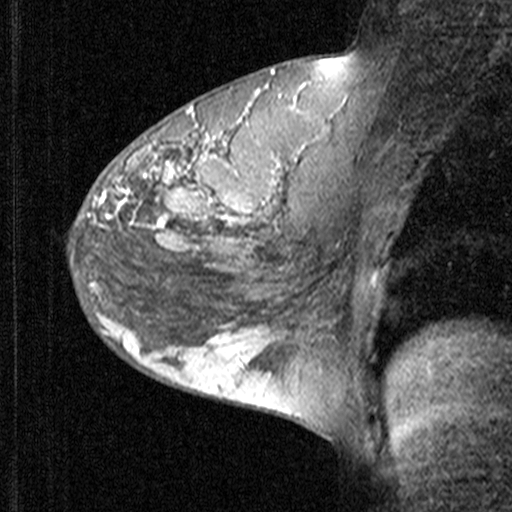
Breast MRI (dynamic contrast-enhanced), one sagittal slice; dynamic contrast-enhanced study with each time point stored as its own series, time point 2 of 3 at this slice position (early post-contrast, ordered by acquisition time); 1.5 T; TE 4.5 ms, TR 11 ms; 3 mm slice thickness; 512 × 512 image matrix, field of view 200 × 200 mm. Female patient, age 27 years. Case-level facts recorded for this patient, not image findings: setting: breast cancer imaged before/during neoadjuvant chemotherapy; receptor status: HR-positive, HER2-negative.
Structures marked on this image (semi-automatic segmentation, software-assisted and operator-edited):
- analysis volume of interest (the breast-tissue region the enhancement analysis was run in; not a lesion): bounding box [x1, y1, x2, y2] px = [68, 146, 165, 239]
- tumour enhancement mask (voxels above the 90 % enhancement threshold inside the analysis volume of interest): [103, 169, 164, 220]